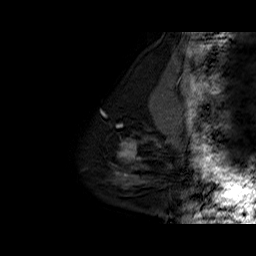
Breast MRI (dynamic contrast-enhanced), one sagittal slice; position 11 of 60 along the scan axis; dynamic contrast-enhanced series, time point 2 of 6 at this slice position (early post-contrast); 1.5 T; TE 6.3 ms, TR 32.5 ms; 256 × 256 image matrix, field of view 200 × 200 mm. Female patient. Case-level facts recorded for this patient, not image findings: setting: breast cancer imaged before/during neoadjuvant chemotherapy; receptor status: triple-negative.
Outlined on this slice (semi-automatic segmentation, software-assisted and operator-edited):
- analysis volume of interest (the breast-tissue region the enhancement analysis was run in; not a lesion): box from (x=110, y=127) to (x=162, y=186) px
- tumour enhancement mask (voxels above the 100 % enhancement threshold inside the analysis volume of interest): (x=119, y=140)–(x=136, y=157)